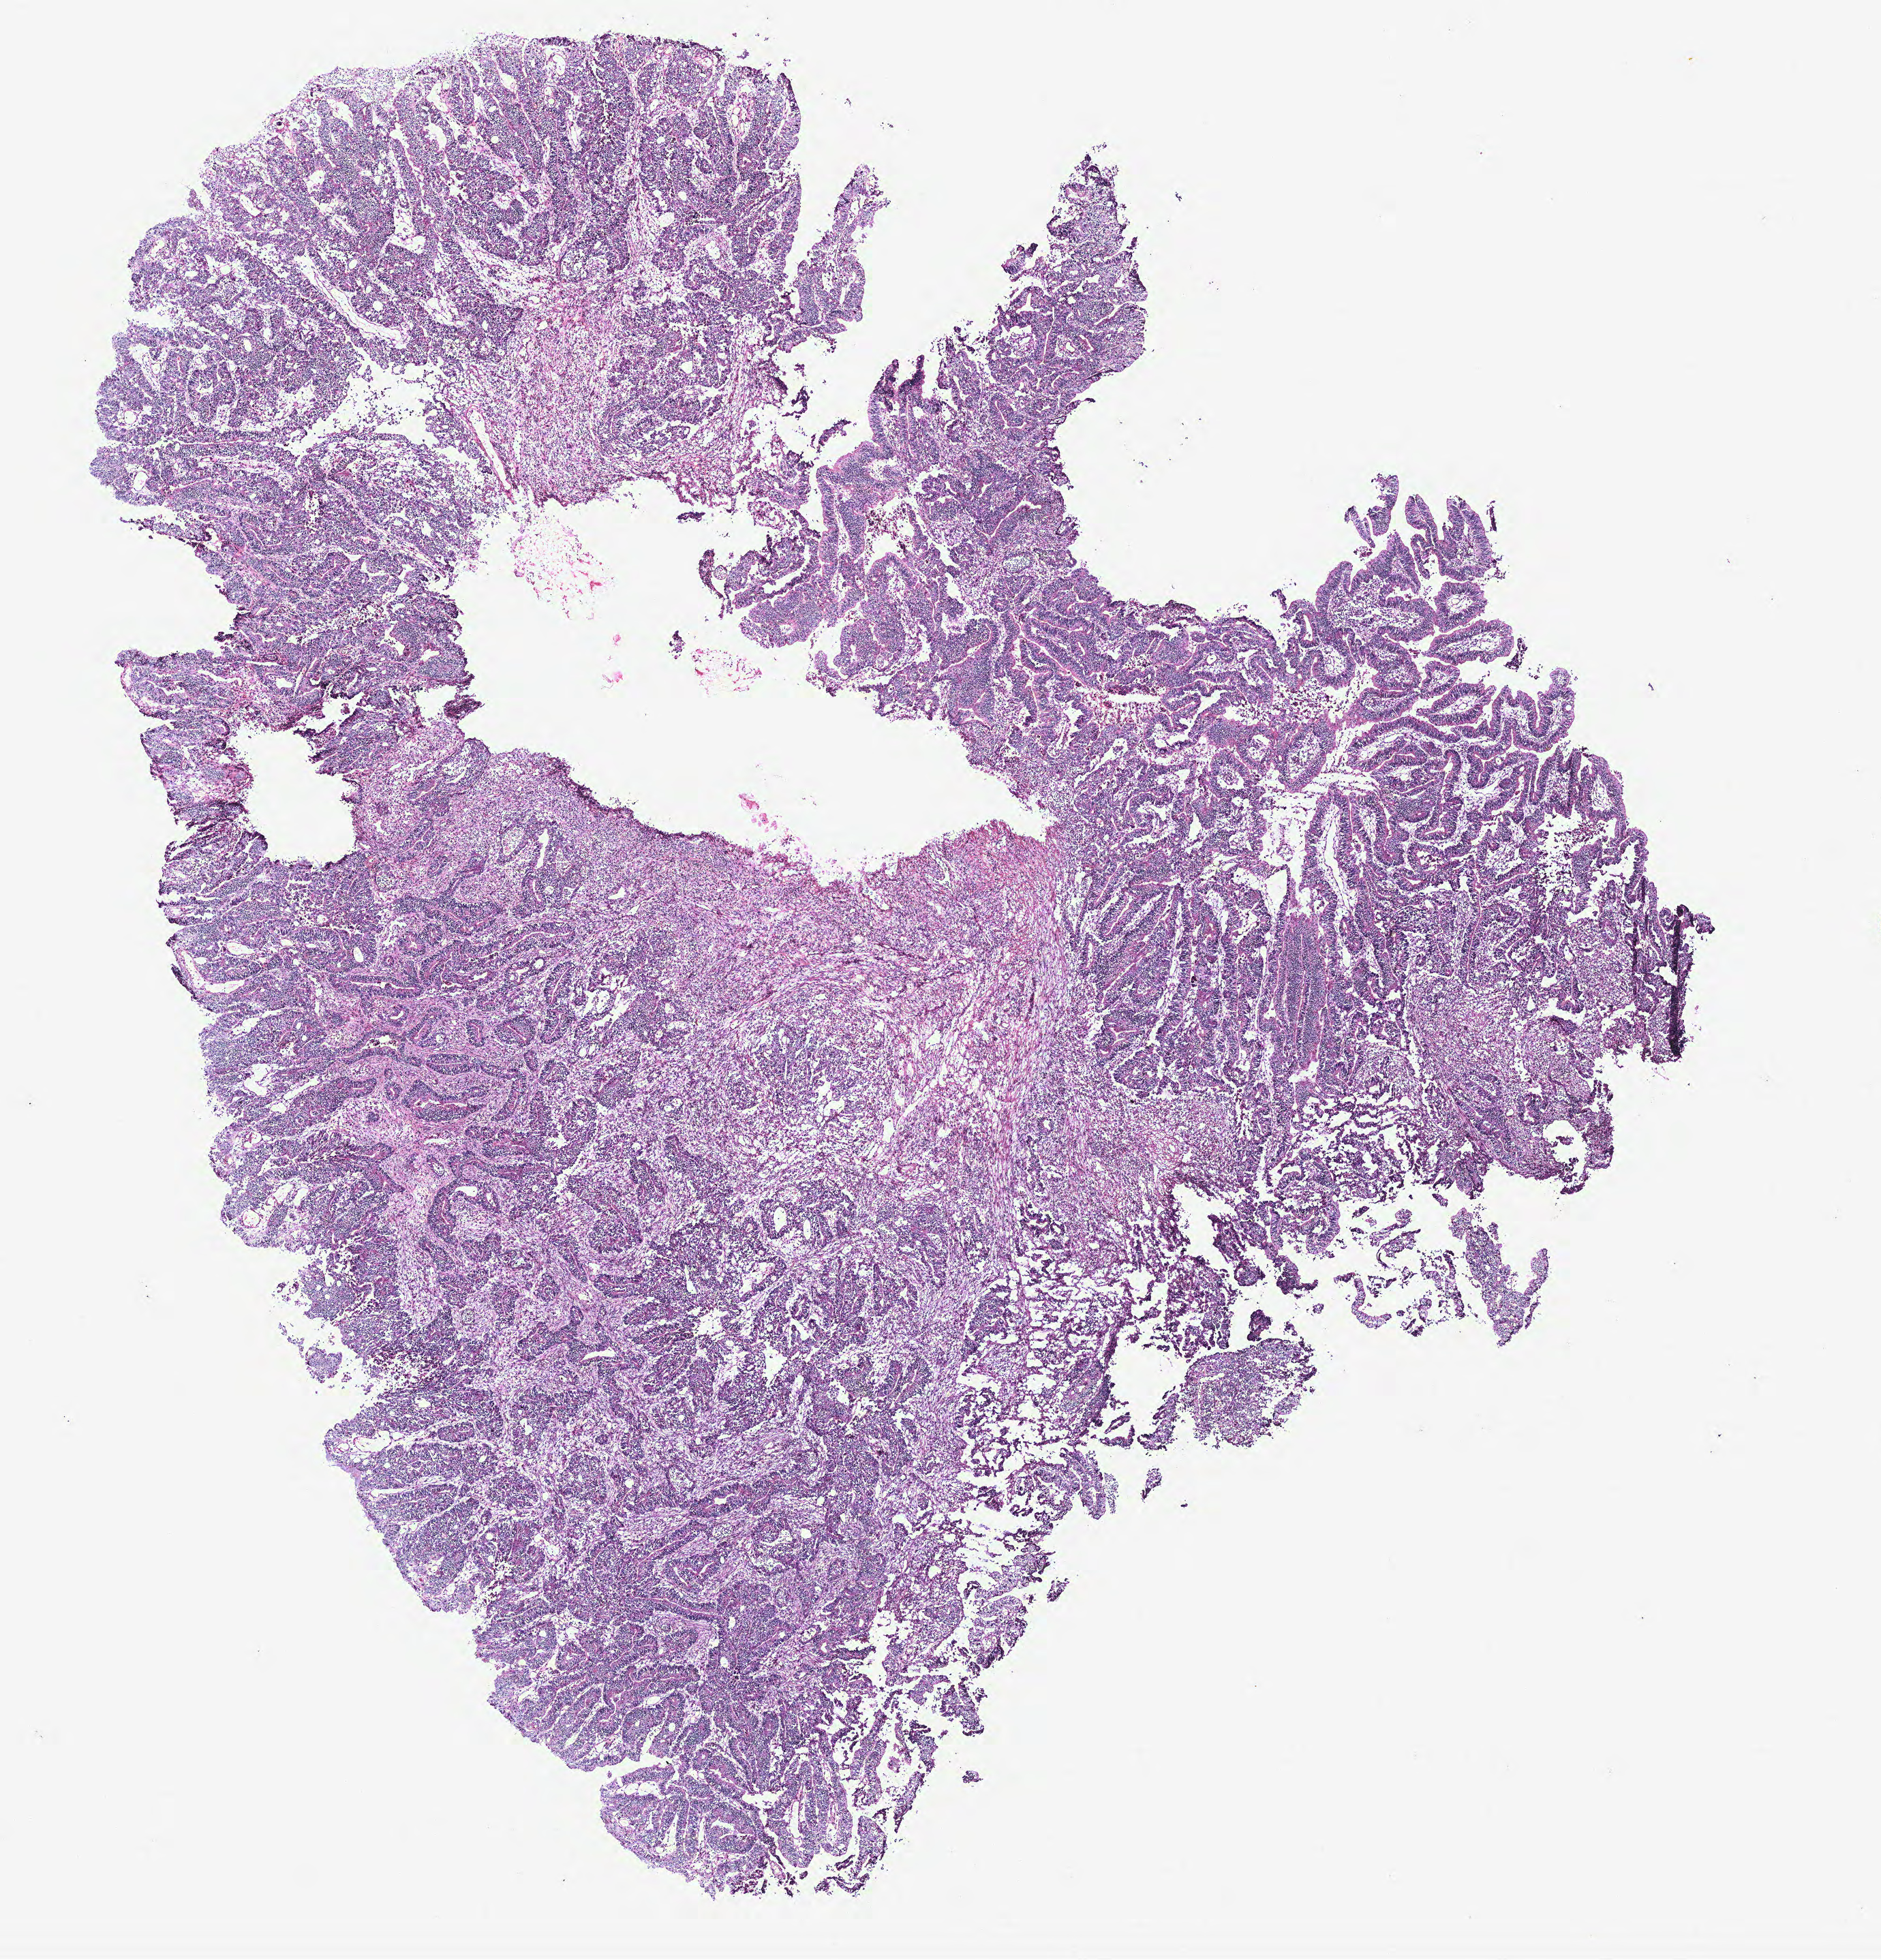
Hematoxylin and eosin (H&E) stained whole-slide image — shown as a low-resolution overview of the whole scanned area (about 11.0 x 11.5 mm, acquisition: 40x scan); colon, tumour tissue. Patient: female, age 52 years.
Primary tumour site (as recorded): colon. AJCC pathologic stage: IIIA. Histologic diagnosis: Adenocarcinoma, NOS.